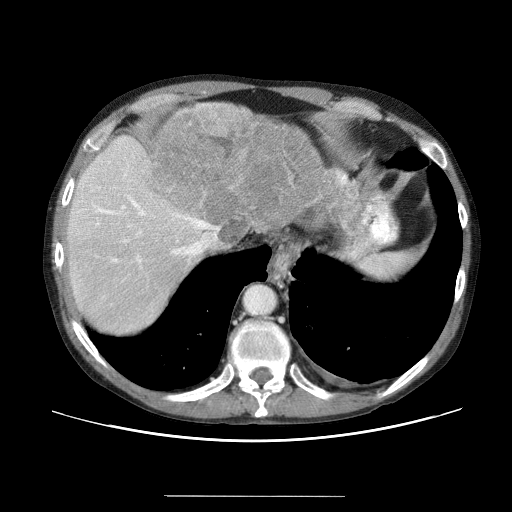
Contrast-enhanced abdominal CT (liver protocol), one axial slice. Position 51 of 69 along the scan axis. Reconstruction kernel STANDARD. 120 kVp. Soft-tissue window (W 400 / L 40 HU). 2.5 mm slice thickness. 512 × 512 image matrix, field of view 380 × 380 mm. From the clinical record (not read from this slice): diagnosis: hepatocellular carcinoma (patient treated with transarterial chemoembolisation; whether this scan precedes or follows treatment is not stated here); TNM stage (as recorded): Stage-IVB; Child-Pugh class: B; tumour nodularity: multinodular.
Annotated regions visible in this slice (semi-automatically segmented with operator editing):
- liver parenchyma outside the tumour (the mass and vessels are separate outlines, so this box may not span the whole liver): box from (x=64, y=108) to (x=362, y=342) px
- mass: (x=141, y=100)–(x=362, y=233)
- liver vessels: (x=96, y=172)–(x=139, y=256)